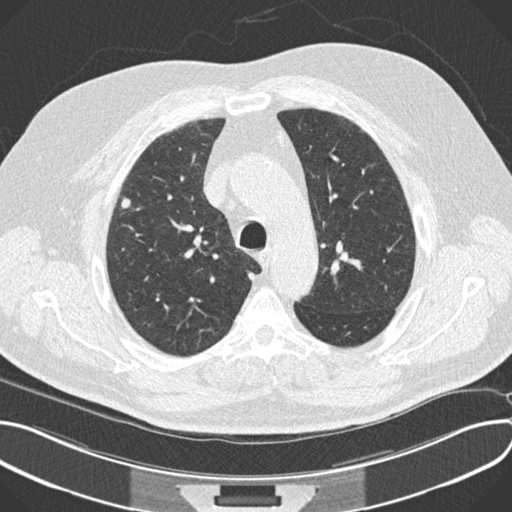
Low-dose screening chest CT, one axial slice. Position 159 of 212 along the scan axis. 120 kVp. Lung window (W 1500 / L -600 HU). 2 mm slice thickness. 512 × 512 image matrix, field of view 380 × 380 mm.
Outlined on this slice (expert manual segmentation):
- lesion 1 (tumor, upper lobe of right lung): bounding box [x1, y1, x2, y2] px = [121, 197, 131, 208]